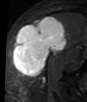
MRI of an extremity soft-tissue mass, one axial slice; position 25 of 48 along the scan axis; STIR; MR volume resampled by the dataset authors to the PET/CT grid (not the native acquisition matrix); 87 × 102 image matrix. Female patient. Case-level facts recorded for this patient, not image findings: histological type: synovial sarcoma; grade: intermediate; site of the primary tumour: right thigh.
Outlined on this slice (expert contour drawn on MRI and transferred to this co-registered scan by the dataset authors):
- gross tumour volume including surrounding oedema: bounding box (x1, y1, x2, y2) in pixels: (13, 15, 68, 76)
- gross tumour volume (mass): (13, 15, 68, 76)